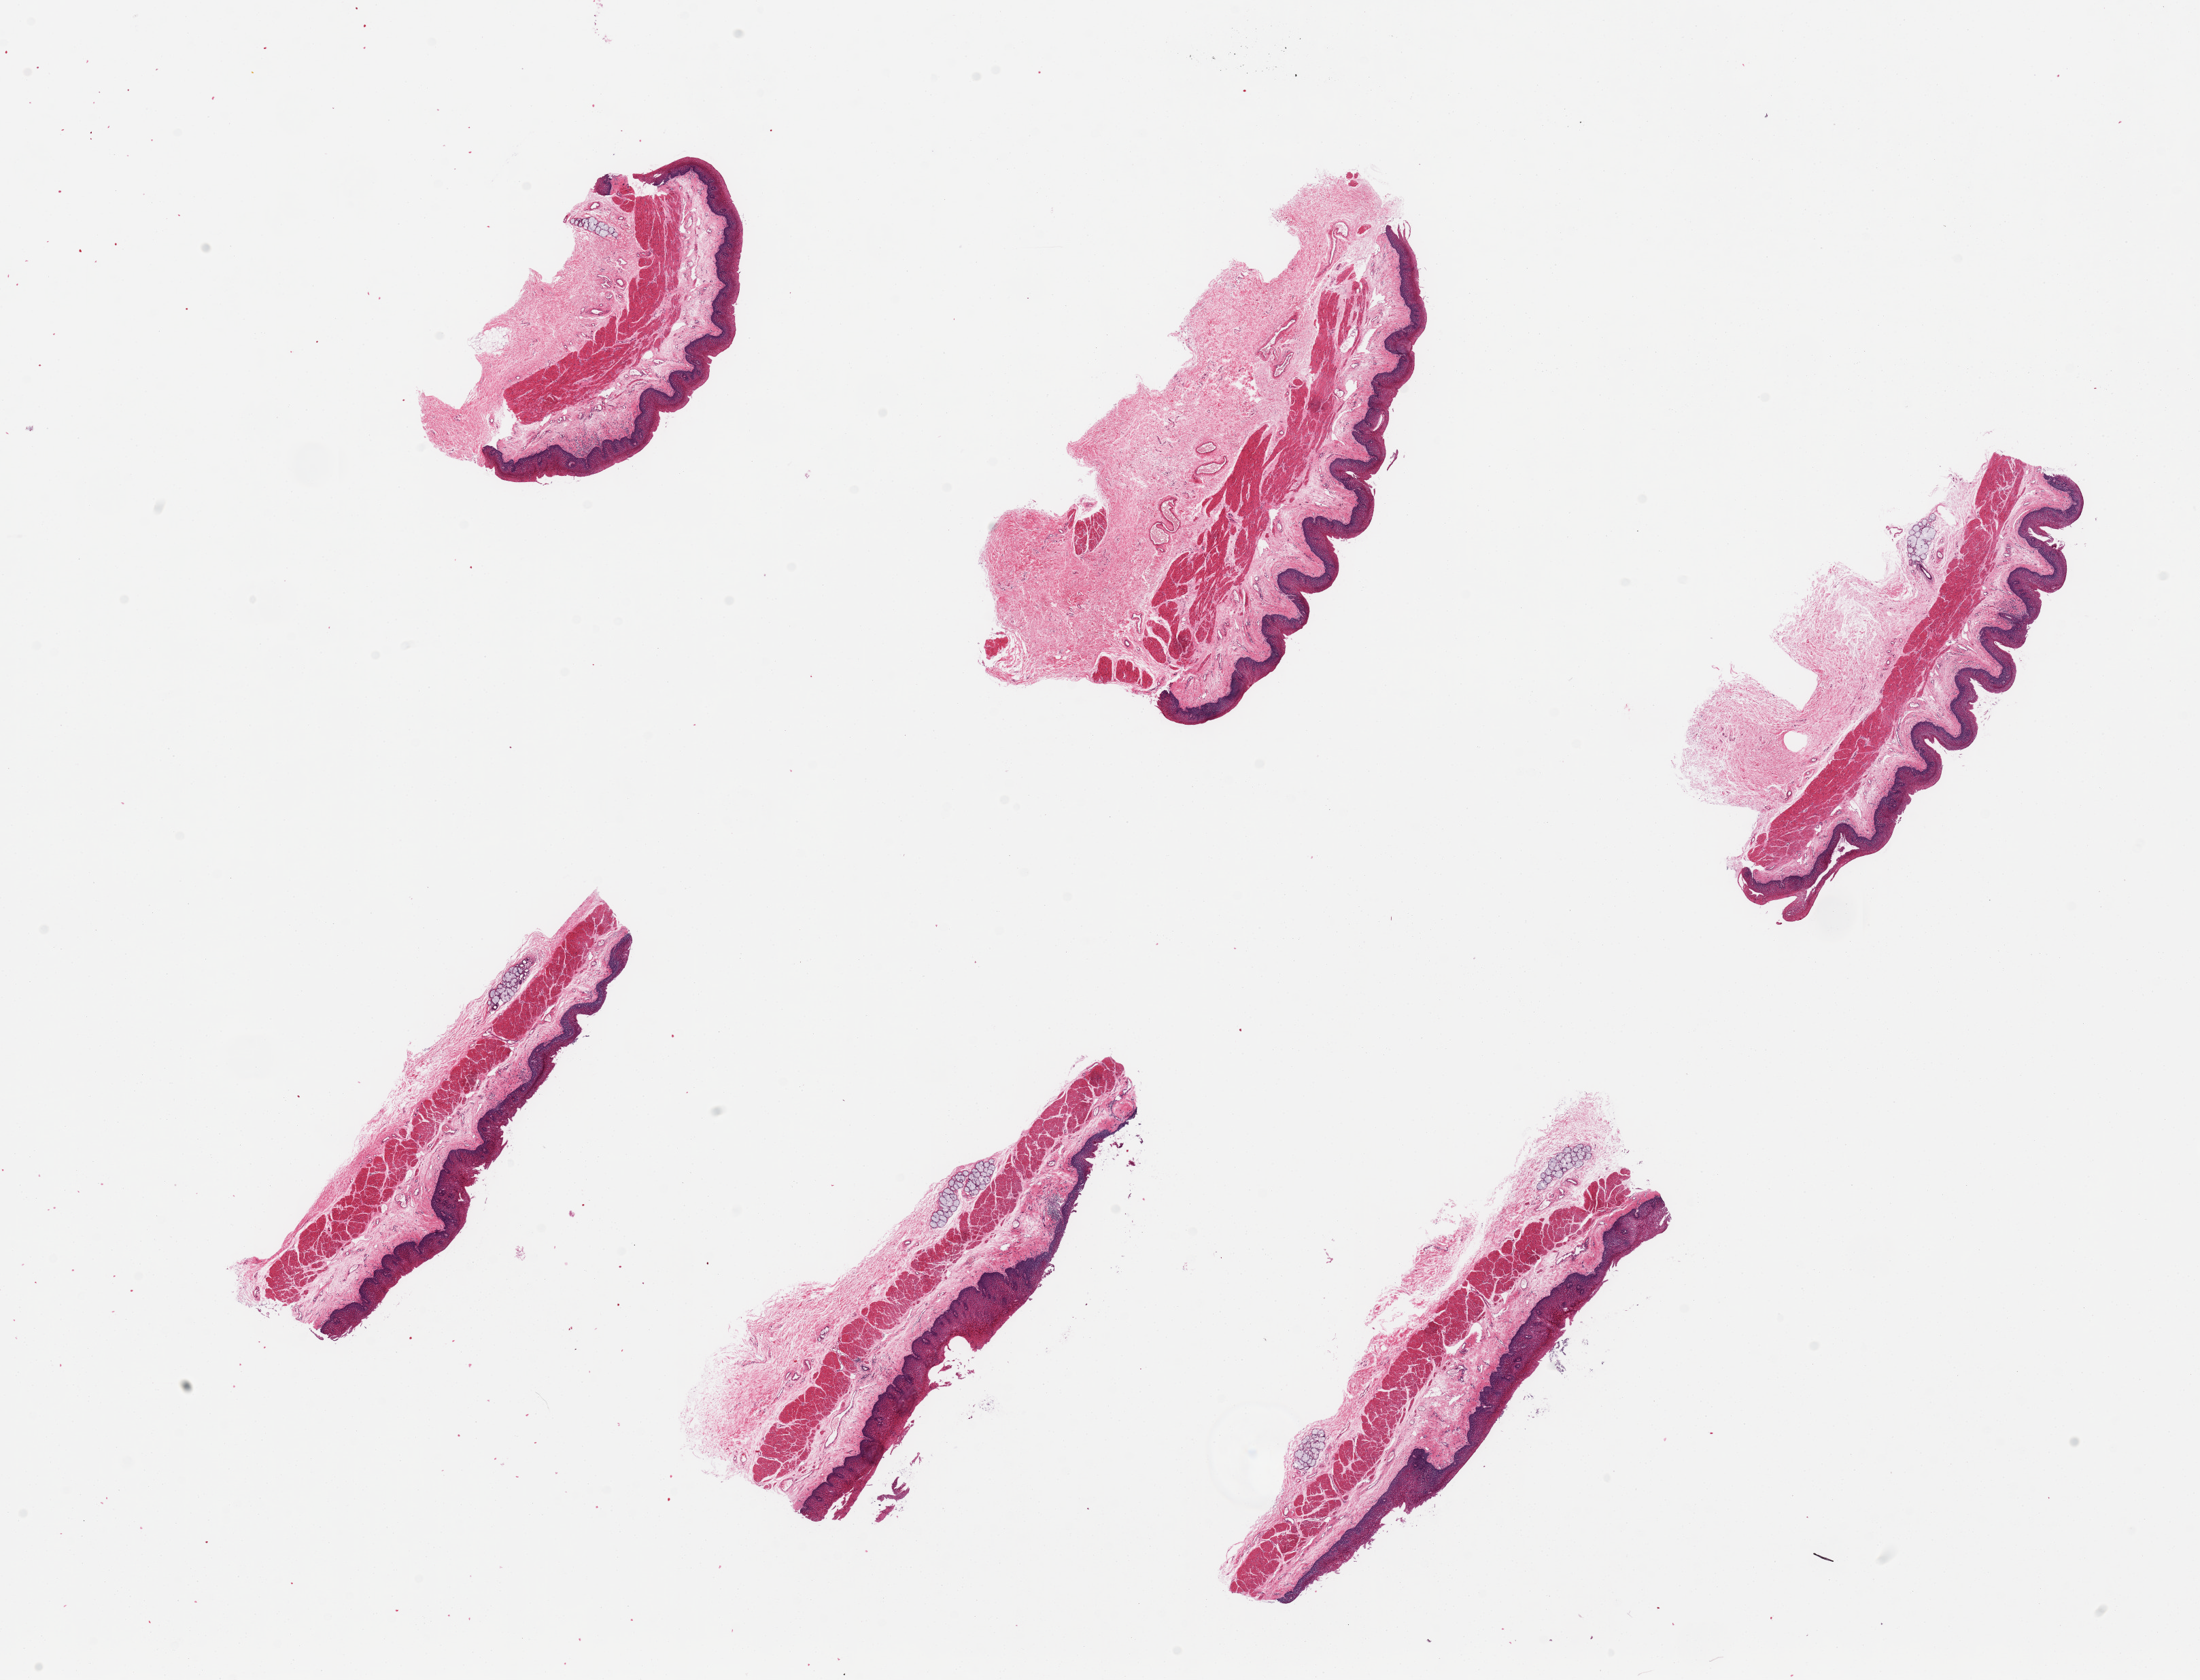
H&E whole-slide image, brightfield — a low-resolution overview of the entire scanned area, about 25.6 x 19.5 mm. PAXgene-fixed, paraffin-embedded tissue. Section of esophageal mucous membrane (target tissue). Donor tissue sample. Donor: female.
Pathologist's review note for this sample: 6 pieces, few submucosal glands (some marked).